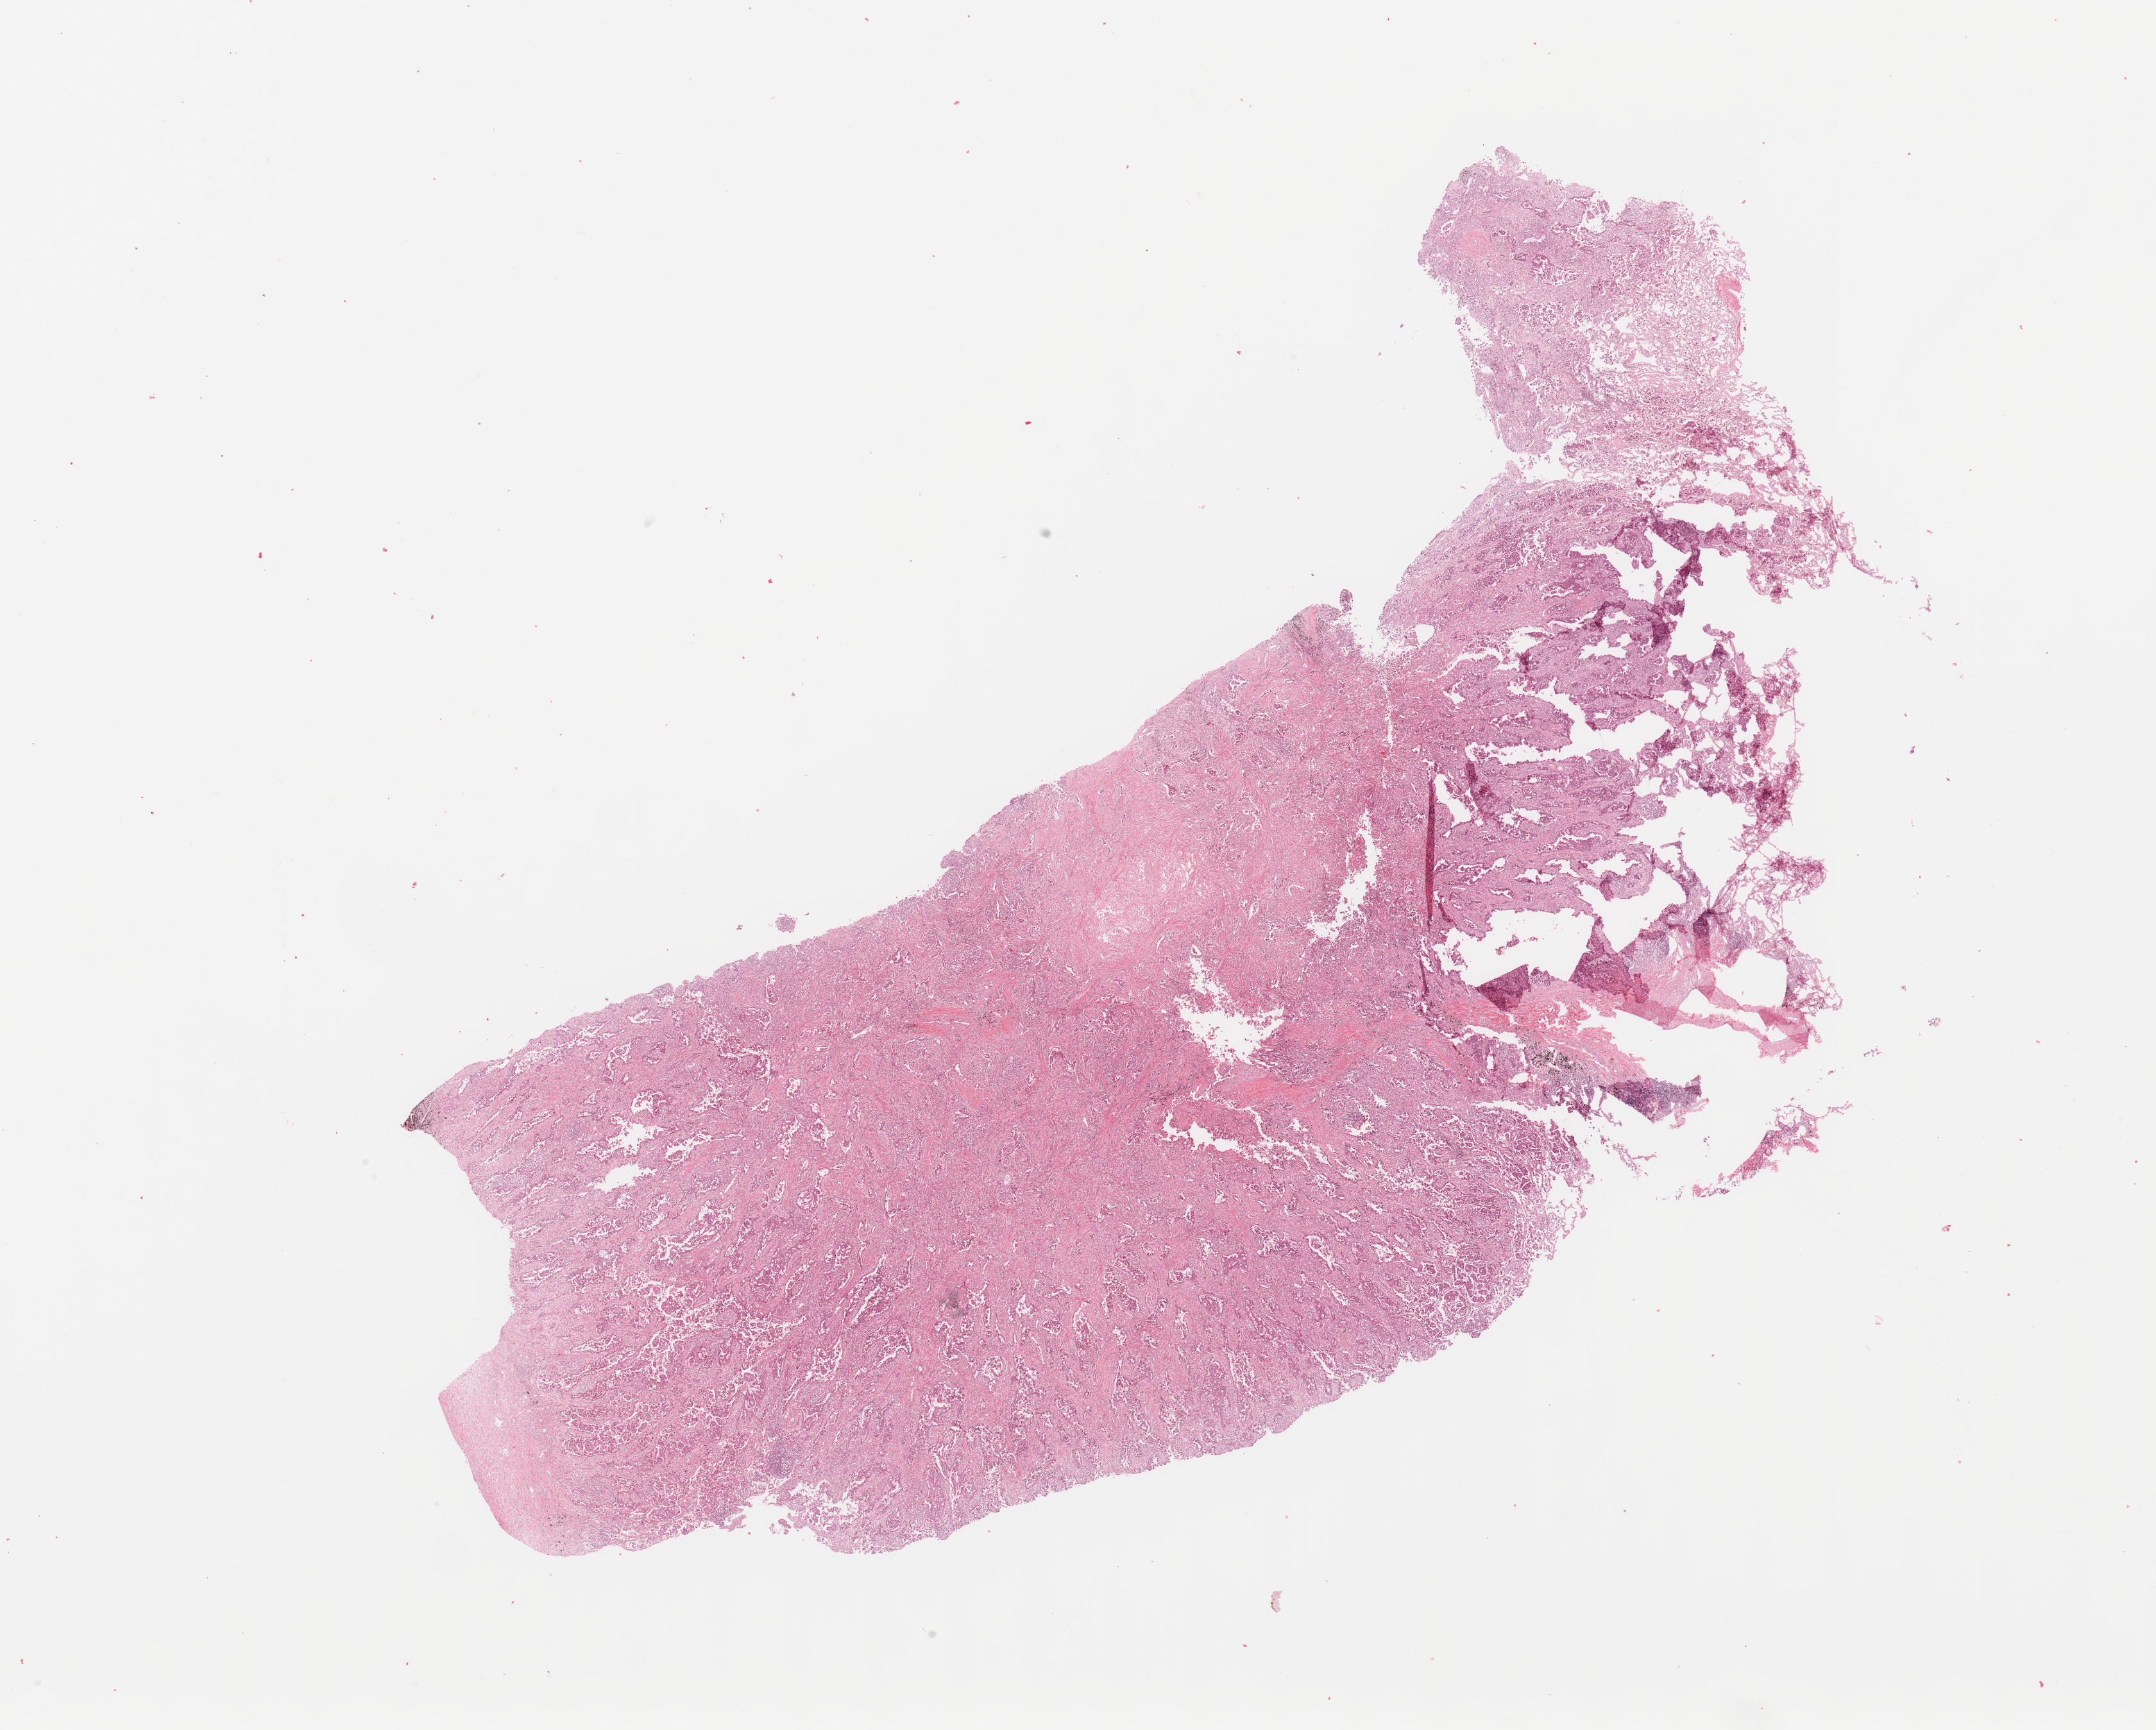
Whole-slide histology image, H&E-stained — a low-resolution overview of the entire scanned area, about 26.6 x 21.3 mm (from a 20x scan), tumour tissue sample, lung. Patient: male, age 62 years. Histologic grade: G3 (poorly differentiated).
- primary tumour site (as recorded): left upper lobe
- AJCC pathologic stage: IIIA
- histologic diagnosis: Adenocarcinoma, NOS